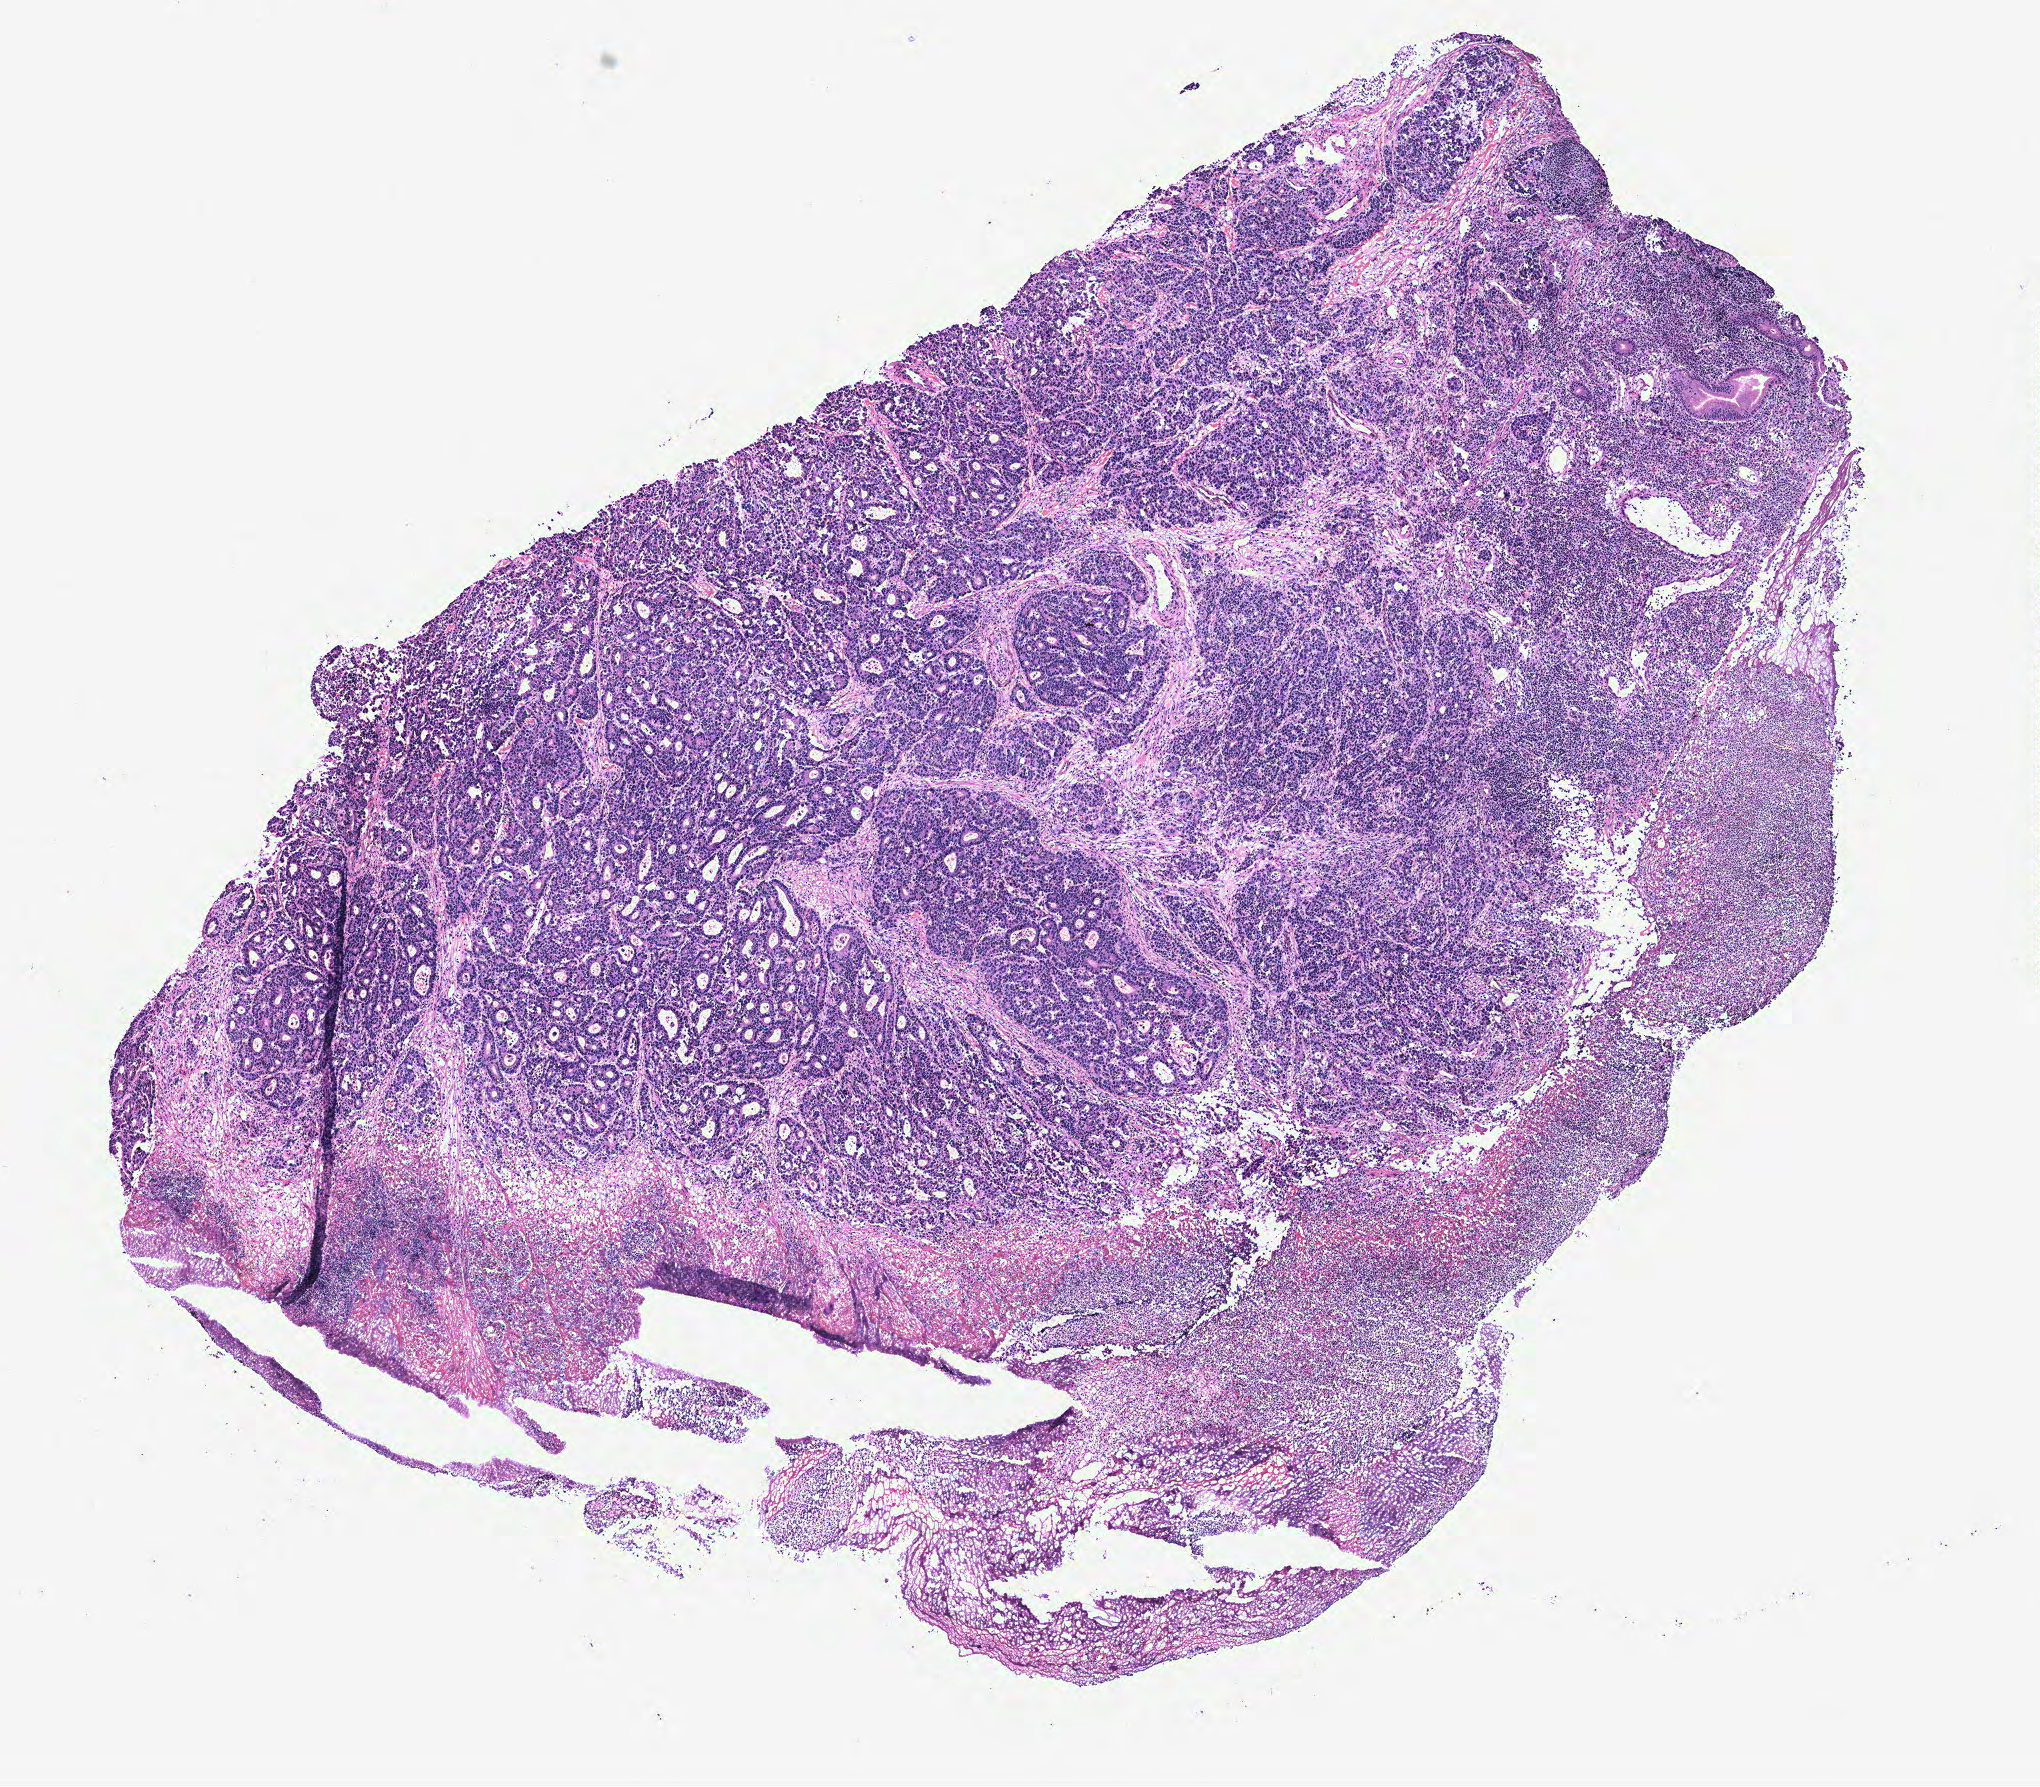
Whole-slide histology image, Hematoxylin and eosin (H&E) stained, a low-resolution overview of the entire scanned area, about 8.2 x 7.2 mm (from a 40x scan); colon, tissue type not recorded.
• patient diagnosis (cohort enrolment): colon cancer (colon)